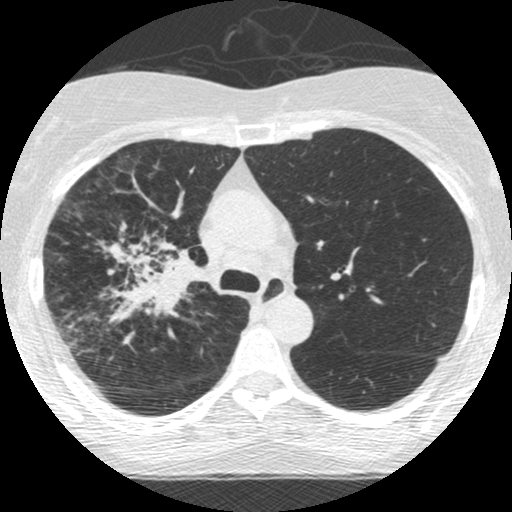
Low-dose screening chest CT, one axial slice; position 177 of 253 along the scan axis; reconstruction kernel STANDARD; lung window (W 1500 / L -600 HU); 1.25 mm slice thickness; 512 × 512 image matrix, field of view 294 × 294 mm.
Annotated regions visible in this slice (expert manual segmentation):
- lesion 2 (tumor, hilum of right lung): bounding box (x1, y1, x2, y2) in pixels: (102, 222, 209, 326)